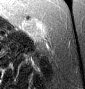
MRI of an extremity soft-tissue mass, one axial slice; position 29 of 46 along the scan axis; T2-weighted fat-saturated; MR volume resampled by the dataset authors to the PET/CT grid (not the native acquisition matrix); 3.27 mm slice thickness; 85 × 89 image matrix, field of view 83 × 87 mm. Female patient. From the clinical record (not read from this slice): histological type: leiomyosarcoma; grade: intermediate; site of the primary tumour: parascapusular.
Outlined on this slice (expert contour drawn on MRI and transferred to this co-registered scan by the dataset authors):
- gross tumour volume including surrounding oedema: bounding box <22,20,46,40> (left, top, right, bottom; pixels)
- gross tumour volume (mass): <24,21,39,36>